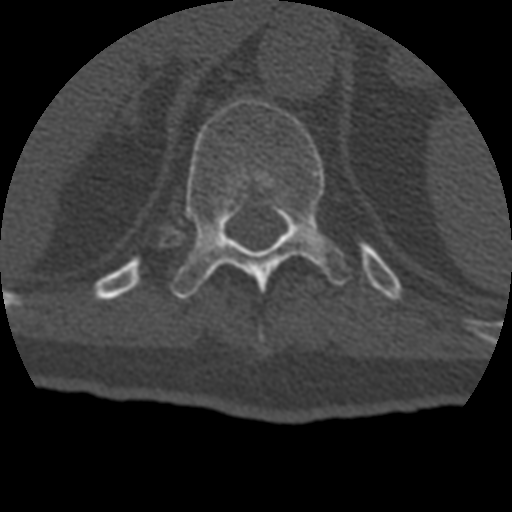
CT including the spine, one axial slice. Slice 198 of 399 in the series (ordered by position). Reconstruction kernel STANDARD. 120 kVp. Bone window (W 1800 / L 400 HU). 1.25 mm slice thickness. 512 × 512 image matrix, field of view 160 × 160 mm. Patient age 69 years. Case-level facts recorded for this patient, not image findings: primary cancer: prostate.
Structures marked on this image (semi-automatic segmentation, software-assisted and operator-edited):
- T11 vertebra: box from (x=171, y=97) to (x=351, y=299) px